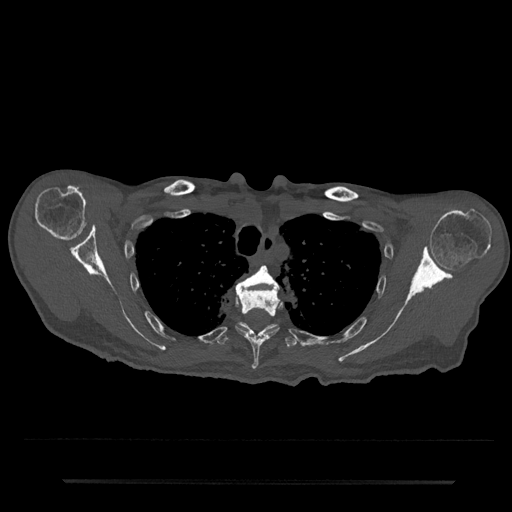
CT including the spine, one axial slice. Slice 616 of 797 in the series (ordered by position). Reconstruction kernel Br40s/3. 120 kVp. Bone window (W 1800 / L 400 HU). 512 × 512 image matrix, field of view 427 × 427 mm. Patient: male, 74 years. Case-level facts recorded for this patient, not image findings: primary cancer: prostate.
Outlined on this slice (semi-automatic segmentation, software-assisted and operator-edited):
- T3 vertebra: bounding box [x1, y1, x2, y2] px = [237, 265, 280, 291]
- T4 vertebra: [236, 287, 282, 370]
- T5 vertebra: [216, 322, 297, 347]